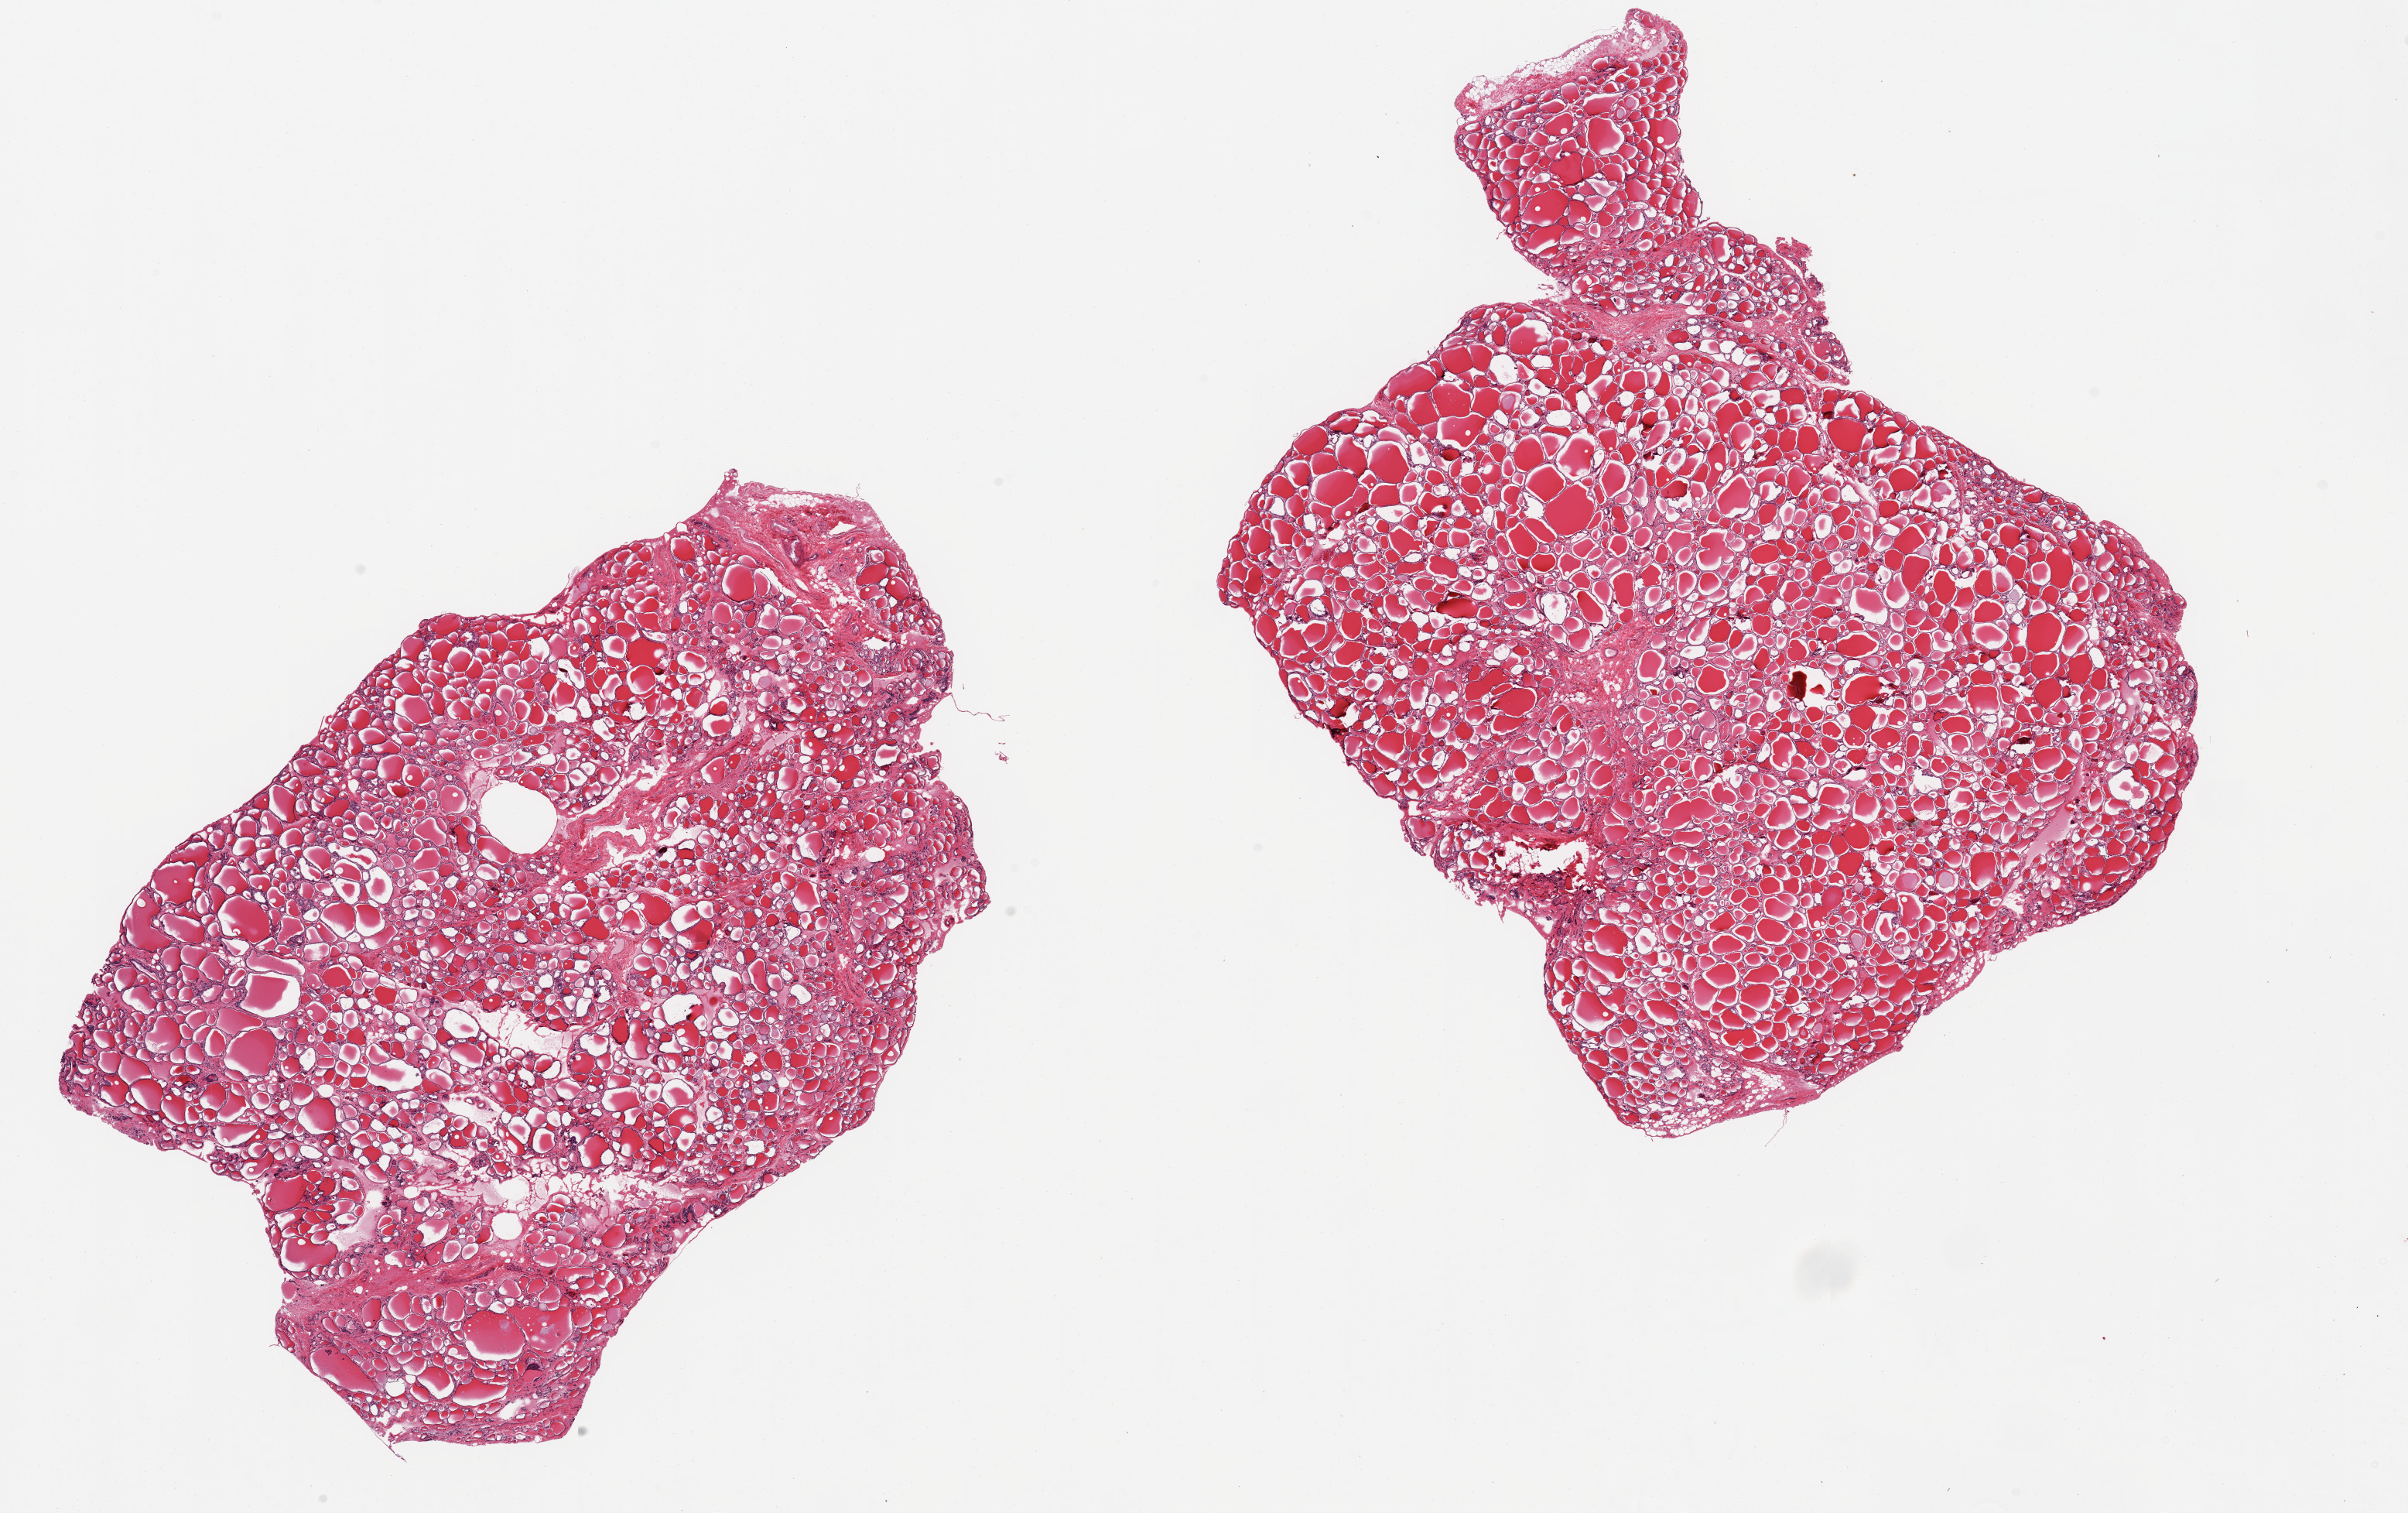
Digitized hematoxylin and eosin (H&E)-stained section, brightfield, whole scanned area (about 24.6 x 15.5 mm, acquisition: 20x scan) shown as a low-resolution overview; PAXgene-fixed paraffin-embedded (PFPE) section; target tissue: thyroid; donor tissue sample. Male donor.
* pathologist's review note for this sample: 2 pieces; mild interstitial fibrosis